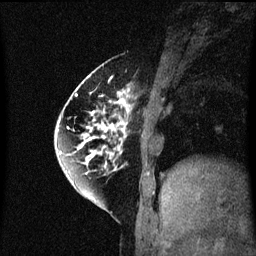
Breast MRI (dynamic contrast-enhanced), one sagittal slice. Slice 19 of 60 in the series (ordered by position). Dynamic contrast-enhanced series, image 2 of 3 at this slice position (ordered by acquisition). 1.5 T. TE 4.2 ms, TR 8.4 ms. 2 mm slice thickness. 256 × 256 image matrix, field of view 200 × 200 mm. Female patient, age 60 years.
Structures marked on this image (semi-automatic segmentation, software-assisted and operator-edited):
- analysis volume of interest (the breast-tissue region the enhancement analysis was run in; not a lesion): bounding box [x1, y1, x2, y2] px = [64, 70, 133, 195]
- tumour enhancement mask (voxels above the 70 % enhancement threshold inside the analysis volume of interest): [64, 72, 133, 195]